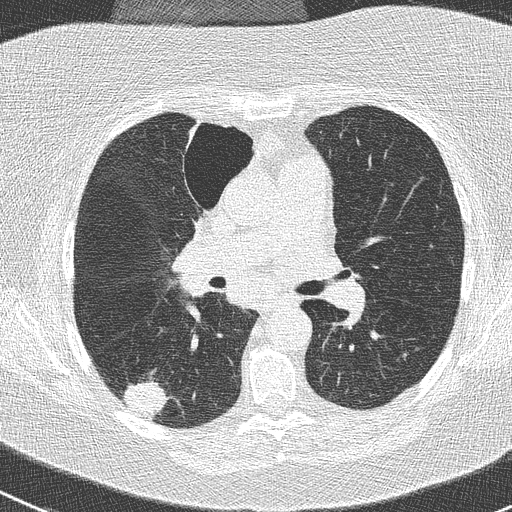
Low-dose screening chest CT, one axial slice; position 150 of 261 along the scan axis; 120 kVp; lung window (W 1500 / L -600 HU); 512 × 512 image matrix, field of view 310 × 310 mm.
Outlined on this slice (manually delineated by an expert):
- lesion 1 (tumor, lower lobe of right lung): bounding box (x1, y1, x2, y2) in pixels: (123, 381, 167, 420)